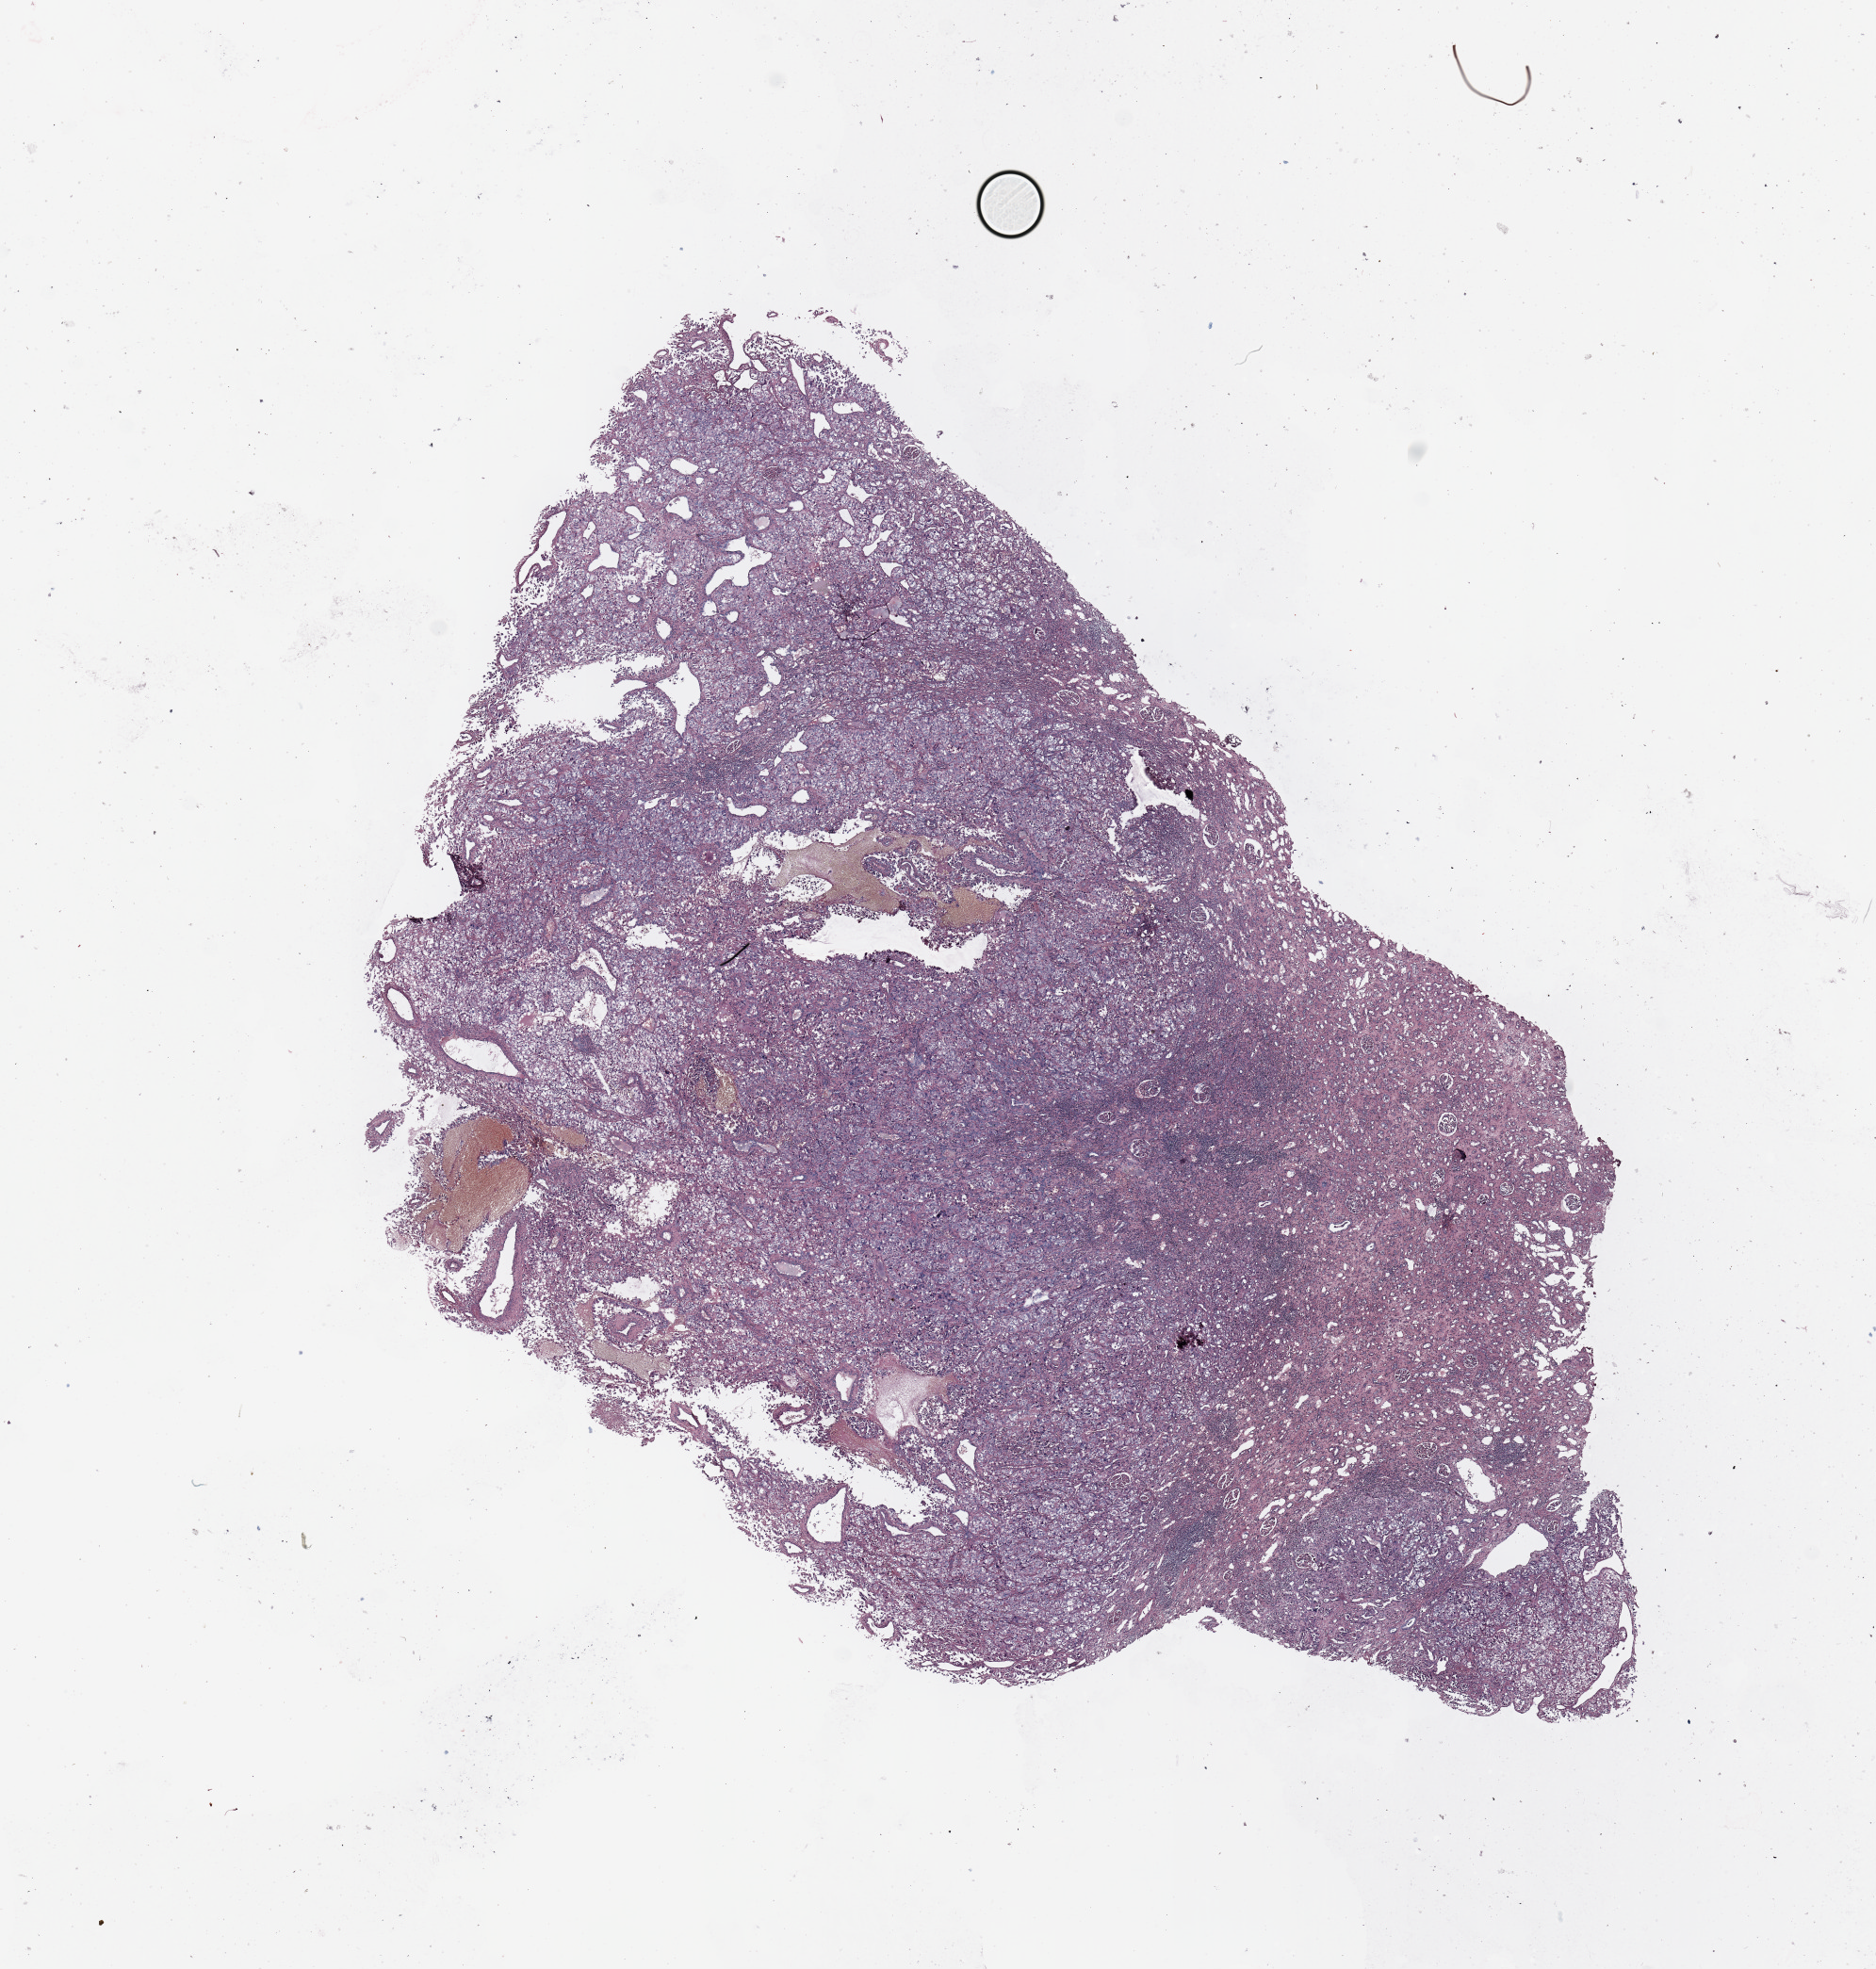
Digitized H&E-stained tissue section (whole slide) — low-resolution overview of the scanned area, about 15.8 x 16.5 mm. Tumour tissue sample, sampled site: kidney. 56-year-old female patient. Histologic grade: G3 (poorly differentiated). Slide review estimates, as recorded: tumour nuclei 60%, necrosis 0%.
Histologic diagnosis: Renal cell carcinoma, NOS. AJCC pathologic stage: IV.